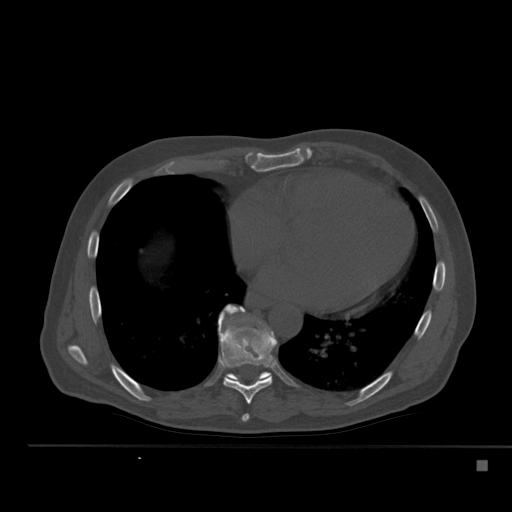
CT including the spine, one axial slice. Position 303 of 517 along the scan axis. Reconstruction kernel Br40s. 120 kVp. Bone window (W 1800 / L 400 HU). 512 × 512 image matrix, field of view 408 × 408 mm. Male patient, age 70 years. Case-level facts recorded for this patient, not image findings: primary cancer: renal; vertebrae with lytic lesions (as recorded): T4, T6, T10, T12, L3, L4, L5.
Outlined on this slice (semi-automatic segmentation, software-assisted and operator-edited):
- T7 vertebra: box from (x=242, y=414) to (x=250, y=422) px
- T8 vertebra: (x=218, y=307)–(x=277, y=404)
- T9 vertebra: (x=225, y=305)–(x=271, y=383)